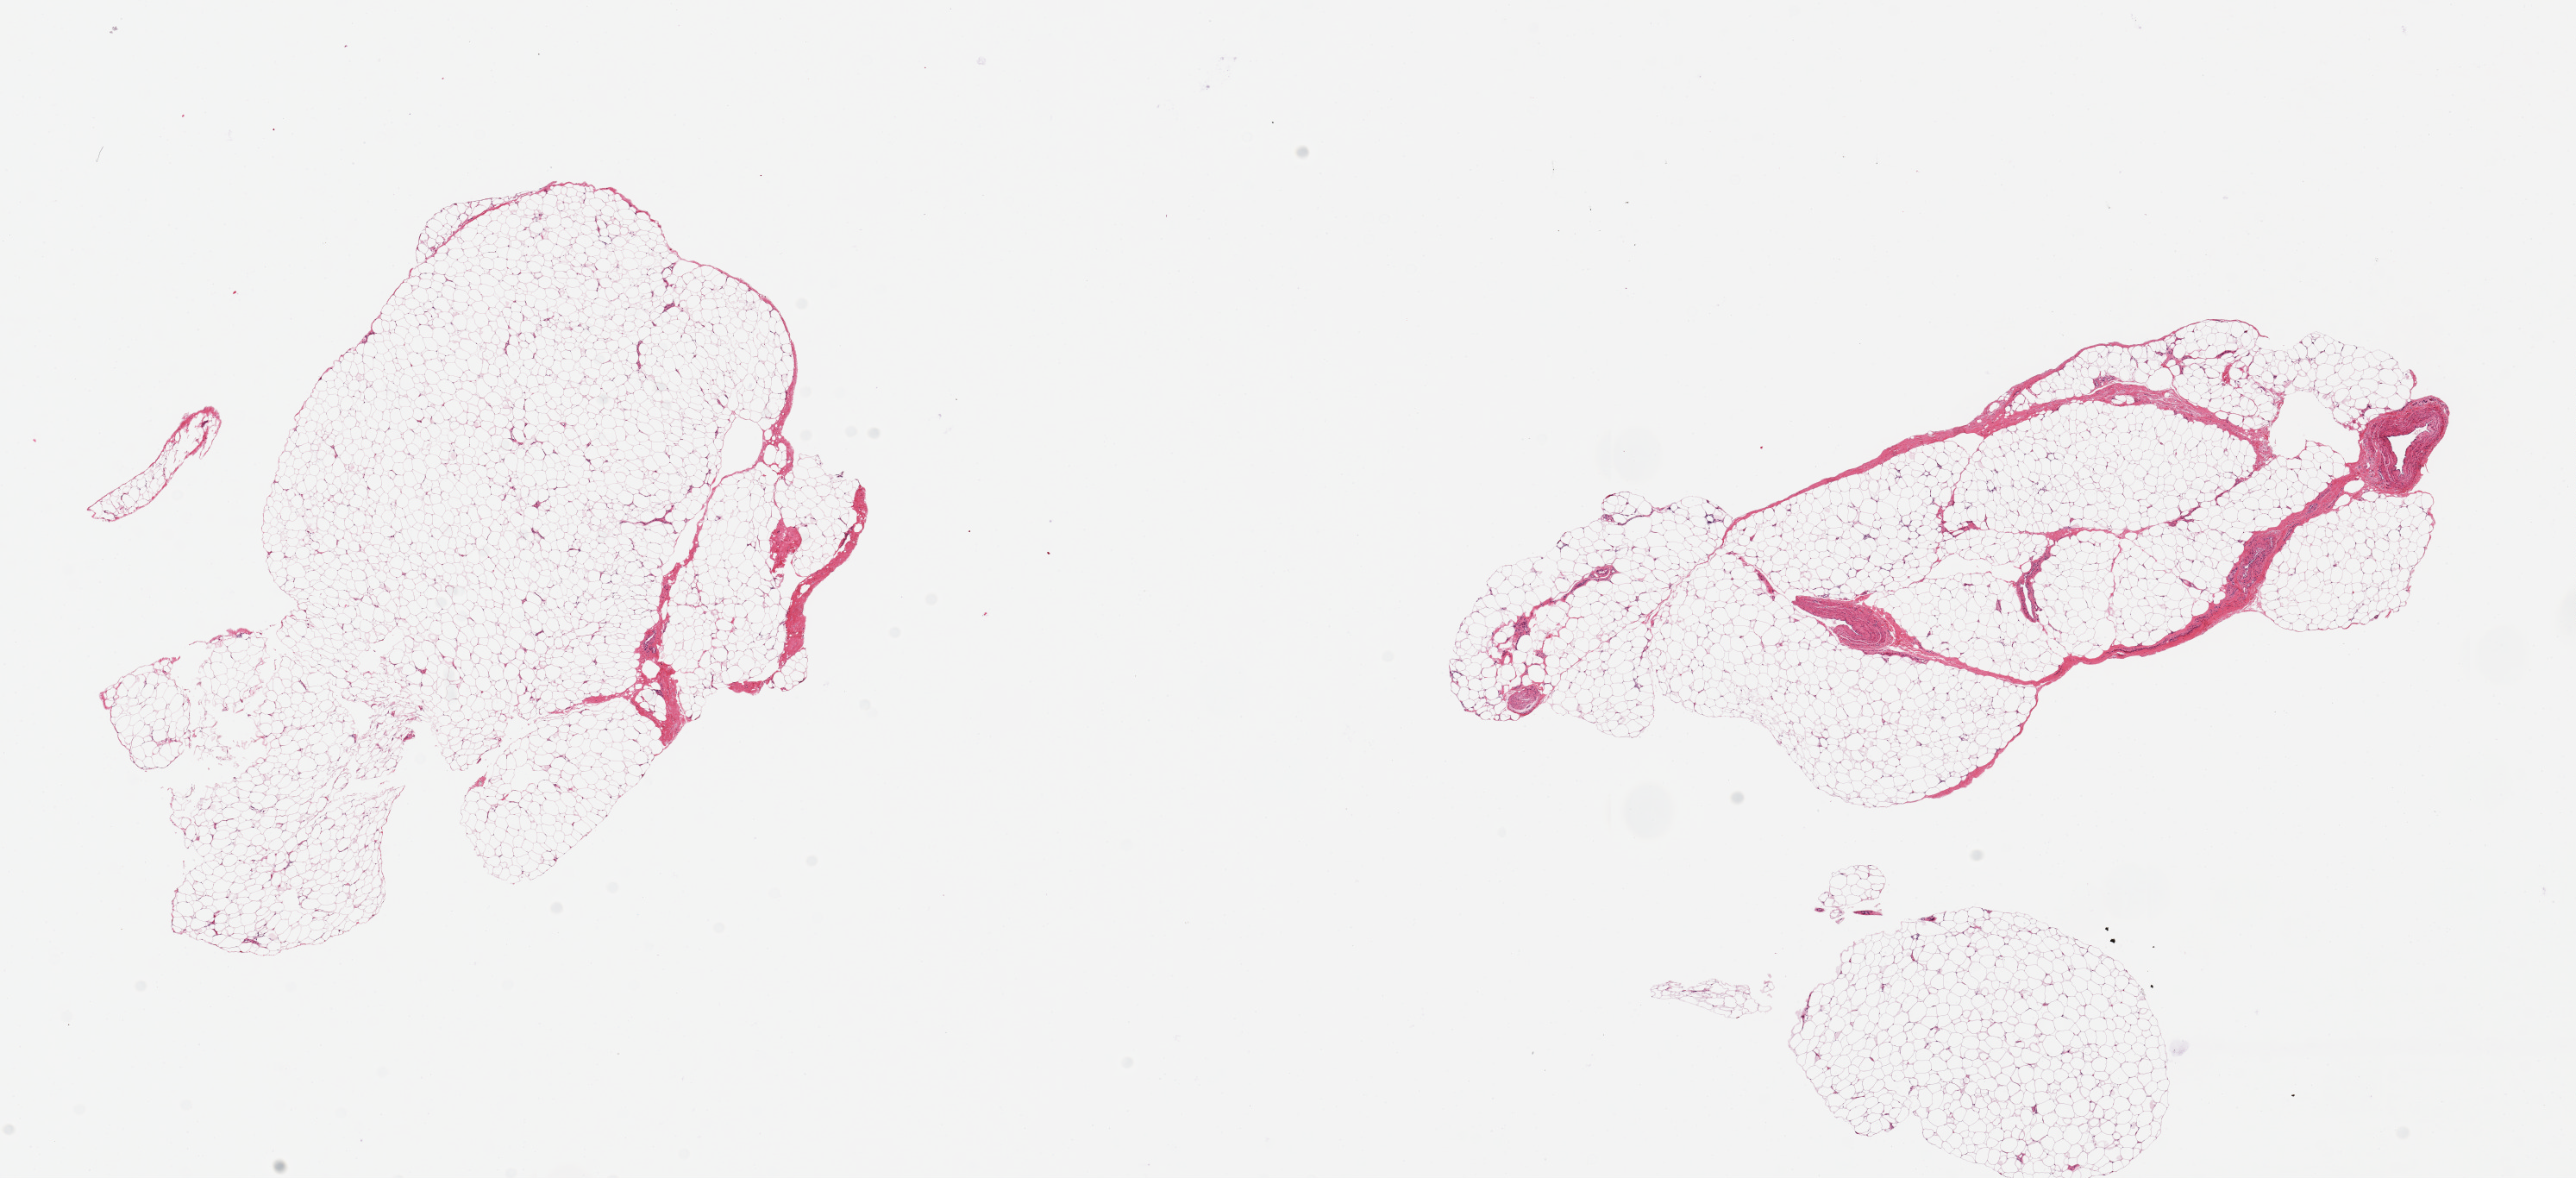
Digitized haematoxylin and eosin-stained section, brightfield — shown as a low-resolution overview of the whole scanned area (about 23.6 x 10.8 mm), PAXgene-fixed paraffin-embedded (PFPE) section, target tissue: adipose tissue, donor tissue sample. Donor: male.
• reviewer comment on this tissue sample: 2 pieces, 8x7 & 9x7mm; No artifacts